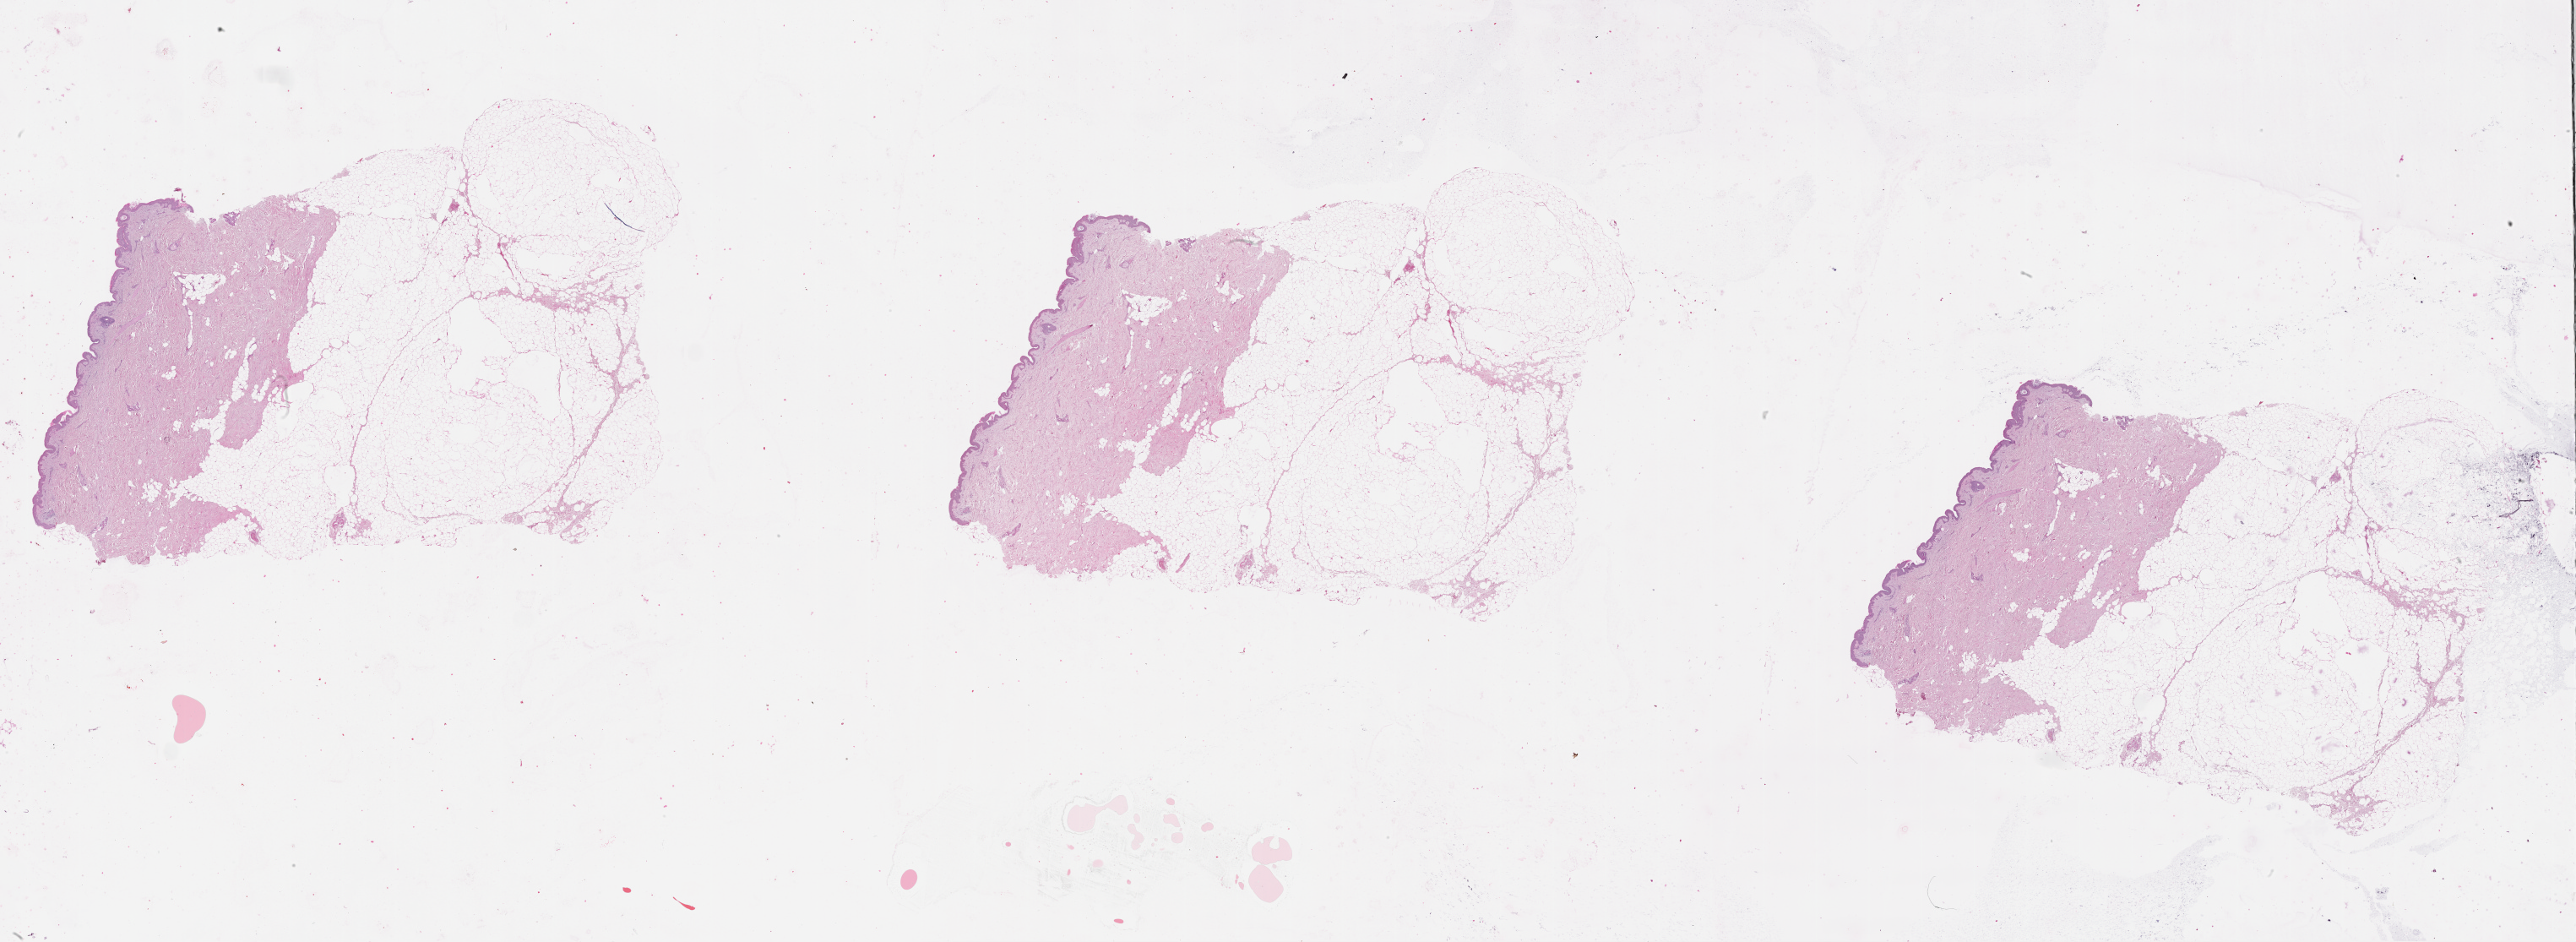
Whole-slide histology image, Hematoxylin and eosin (H&E) stained, a low-resolution overview of the entire scanned area, about 49.1 x 18.0 mm (from a 20x scan), normal (non-tumour) tissue sample, sampled site: chest. Patient: male, age 62 years.
• this section: normal (non-tumour) tissue from the same patient
• patient diagnosis: Malignant melanoma, NOS